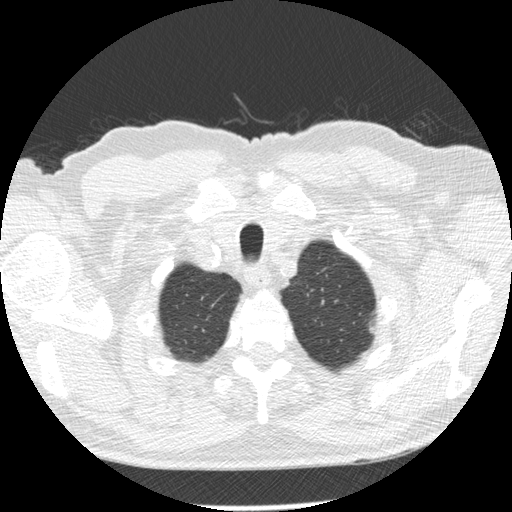
Chest CT (low-dose screening protocol), one axial image; second annual screen; lung window (W 1500 / L -600 HU); 2.5 mm slice thickness; standard (soft-tissue) reconstruction kernel (STANDARD); slice 26 of 276 in the series; 512 × 512 image matrix, field of view 360 × 360 mm. Male participant, aged 73 years at enrolment.
- Lesion marked by an expert reader, bounding box [x1, y1, x2, y2] px = [353, 302, 395, 348].
- No non-calcified nodule or mass ≥4 mm was recorded by the screening reader at this exam.
- Official screen result: negative screen, minor abnormalities not suspicious for lung cancer.